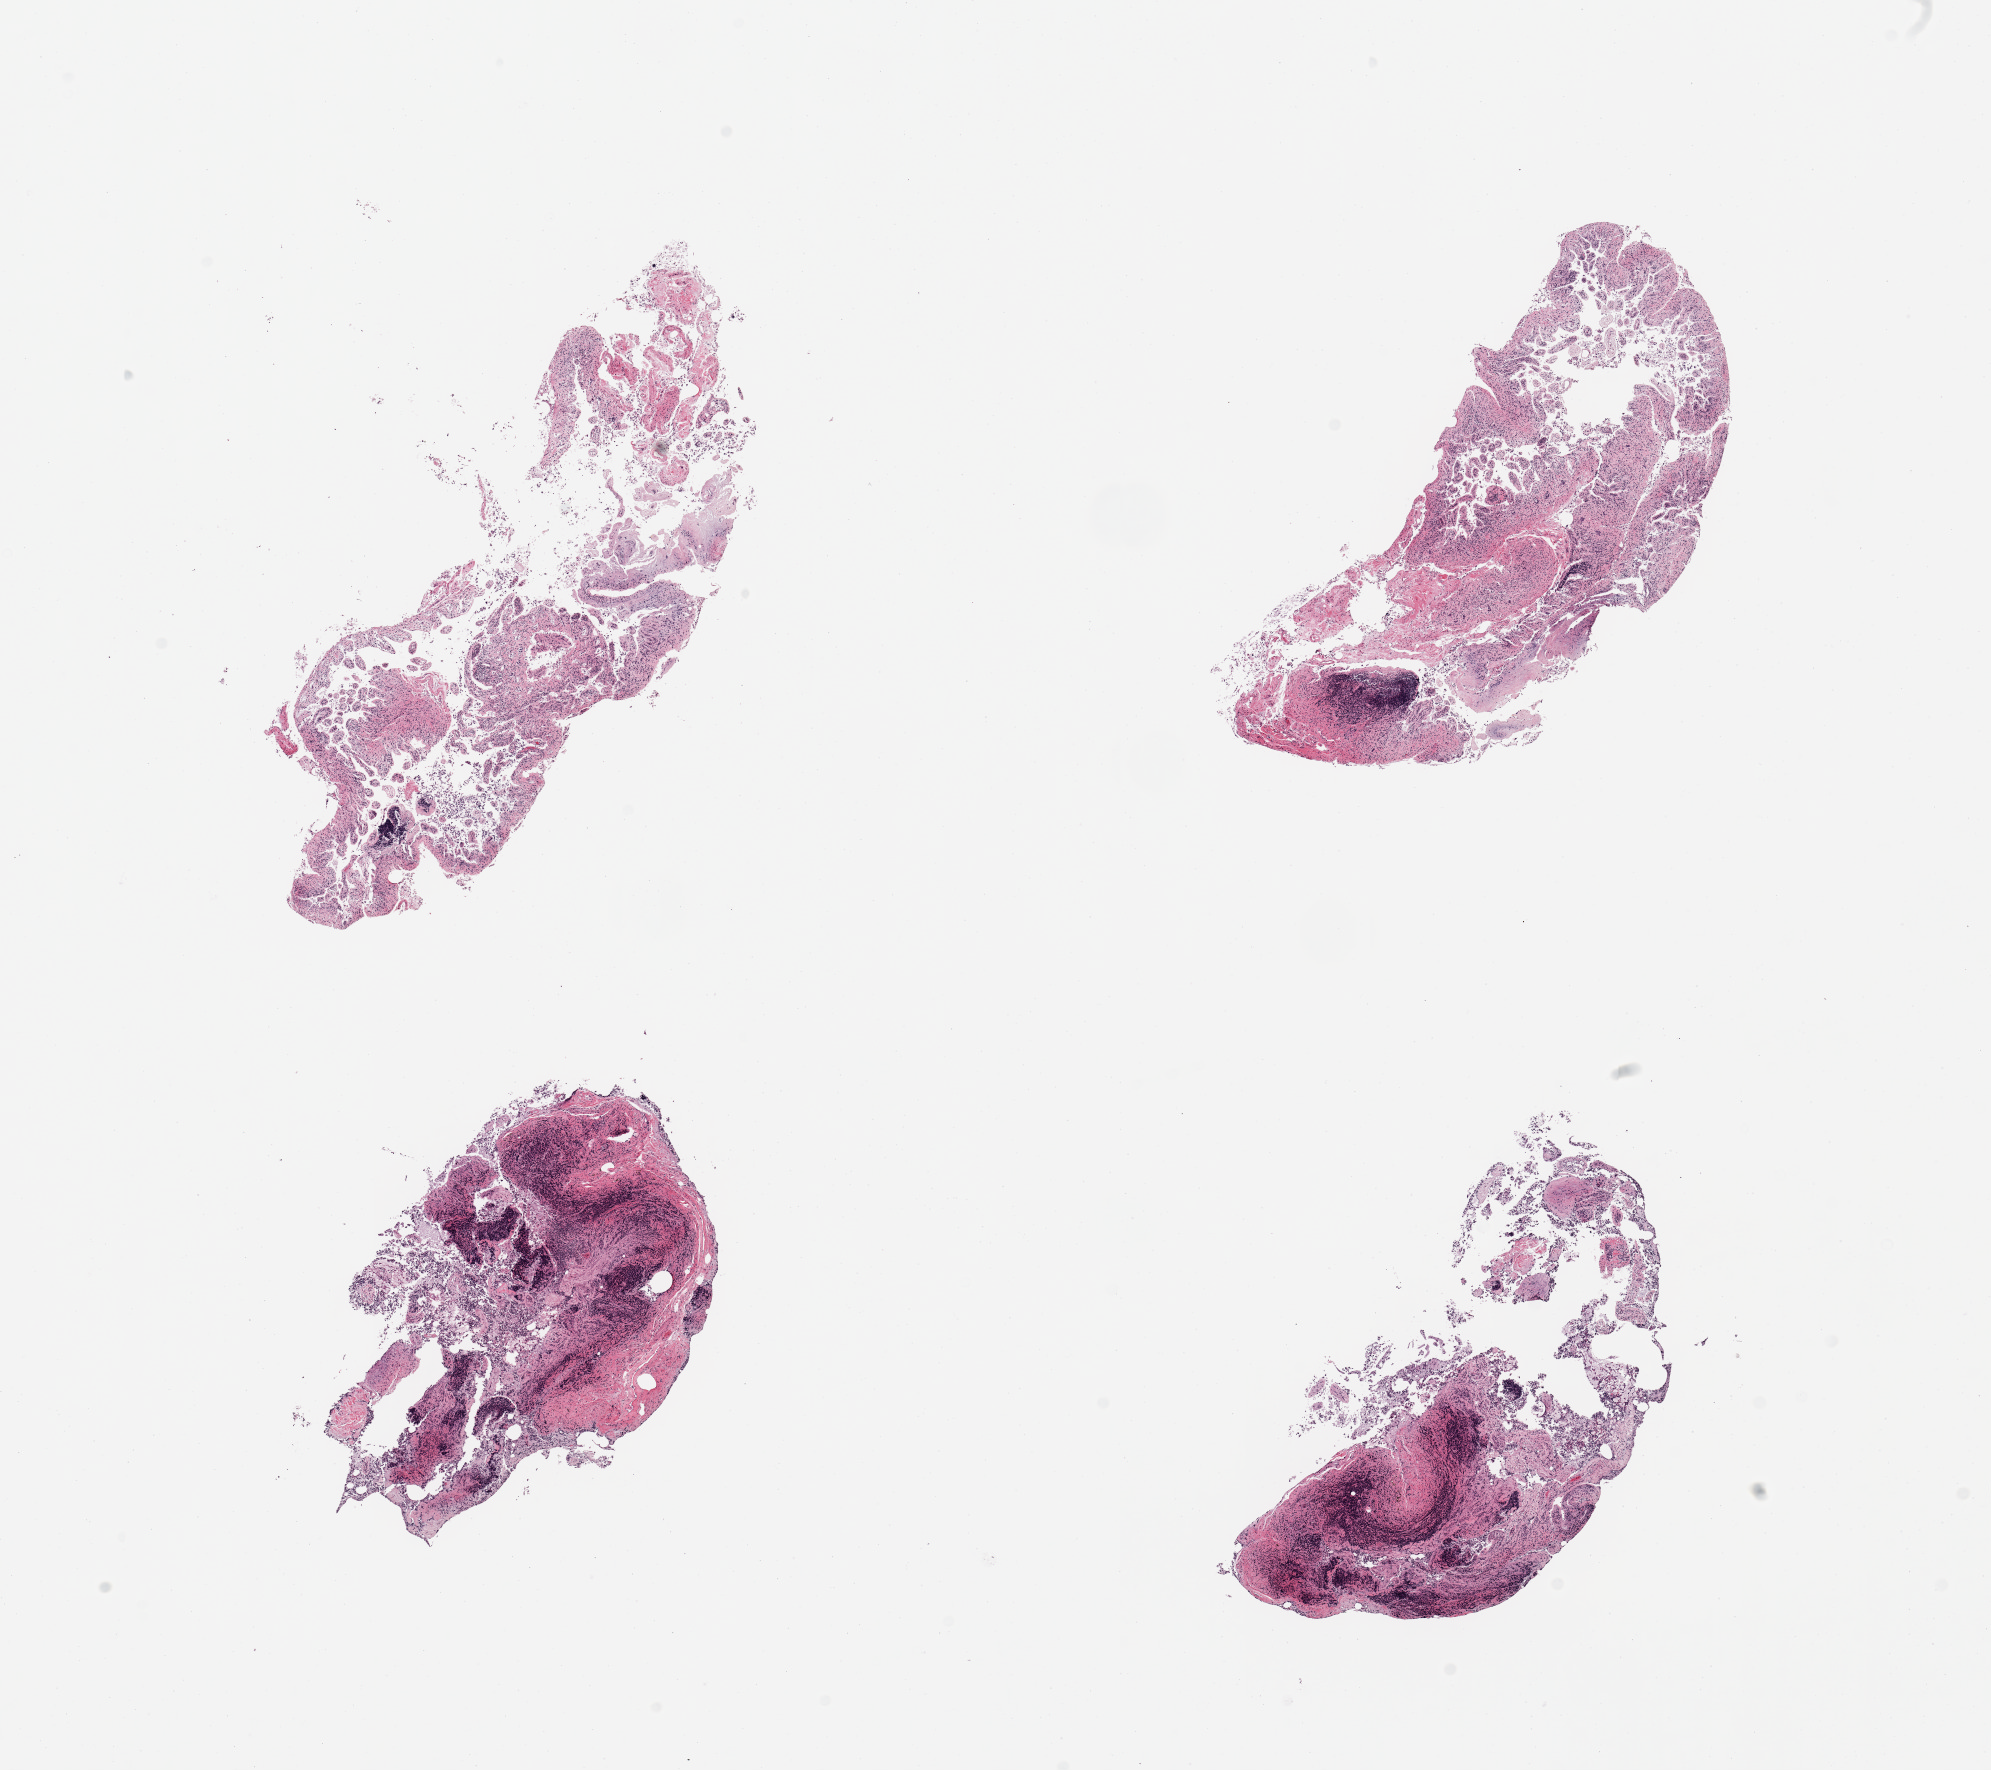
Haematoxylin and eosin whole-slide image — a low-resolution overview of the entire scanned area, about 15.8 x 14.0 mm (slide scanned at 20x), PAXgene-fixed paraffin-embedded (PFPE) section, sampled site (target tissue): ileum, tissue donor sample. Donor: female.
* reviewer comment on this tissue sample: 4 pieces; autolyzed mucosa with some residual lymphoid aggregates ~30% of tissue